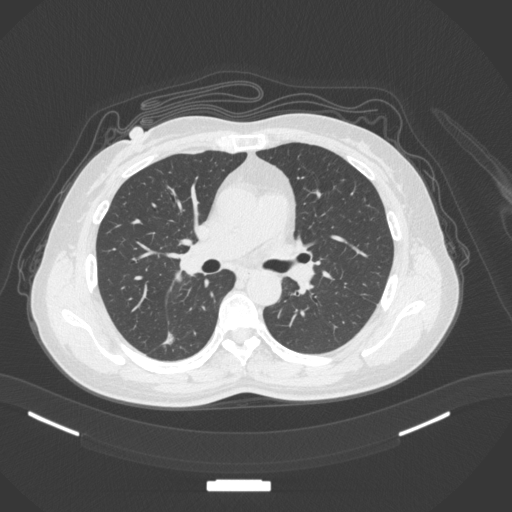
Chest CT, one axial slice; position 179 of 352 along the scan axis; reconstruction kernel B31f; lung window (W 1500 / L -600 HU); 512 × 512 image matrix. Patient: female, 55 years. Case-level facts recorded for this patient, not image findings: clinical TNM (as recorded): T1c N1 M0.
Structures marked on this image (bounding box drawn by a radiologist):
- lung tumour (recorded histology: adenocarcinoma): bounding box (x1, y1, x2, y2) in pixels: (156, 330, 179, 348)